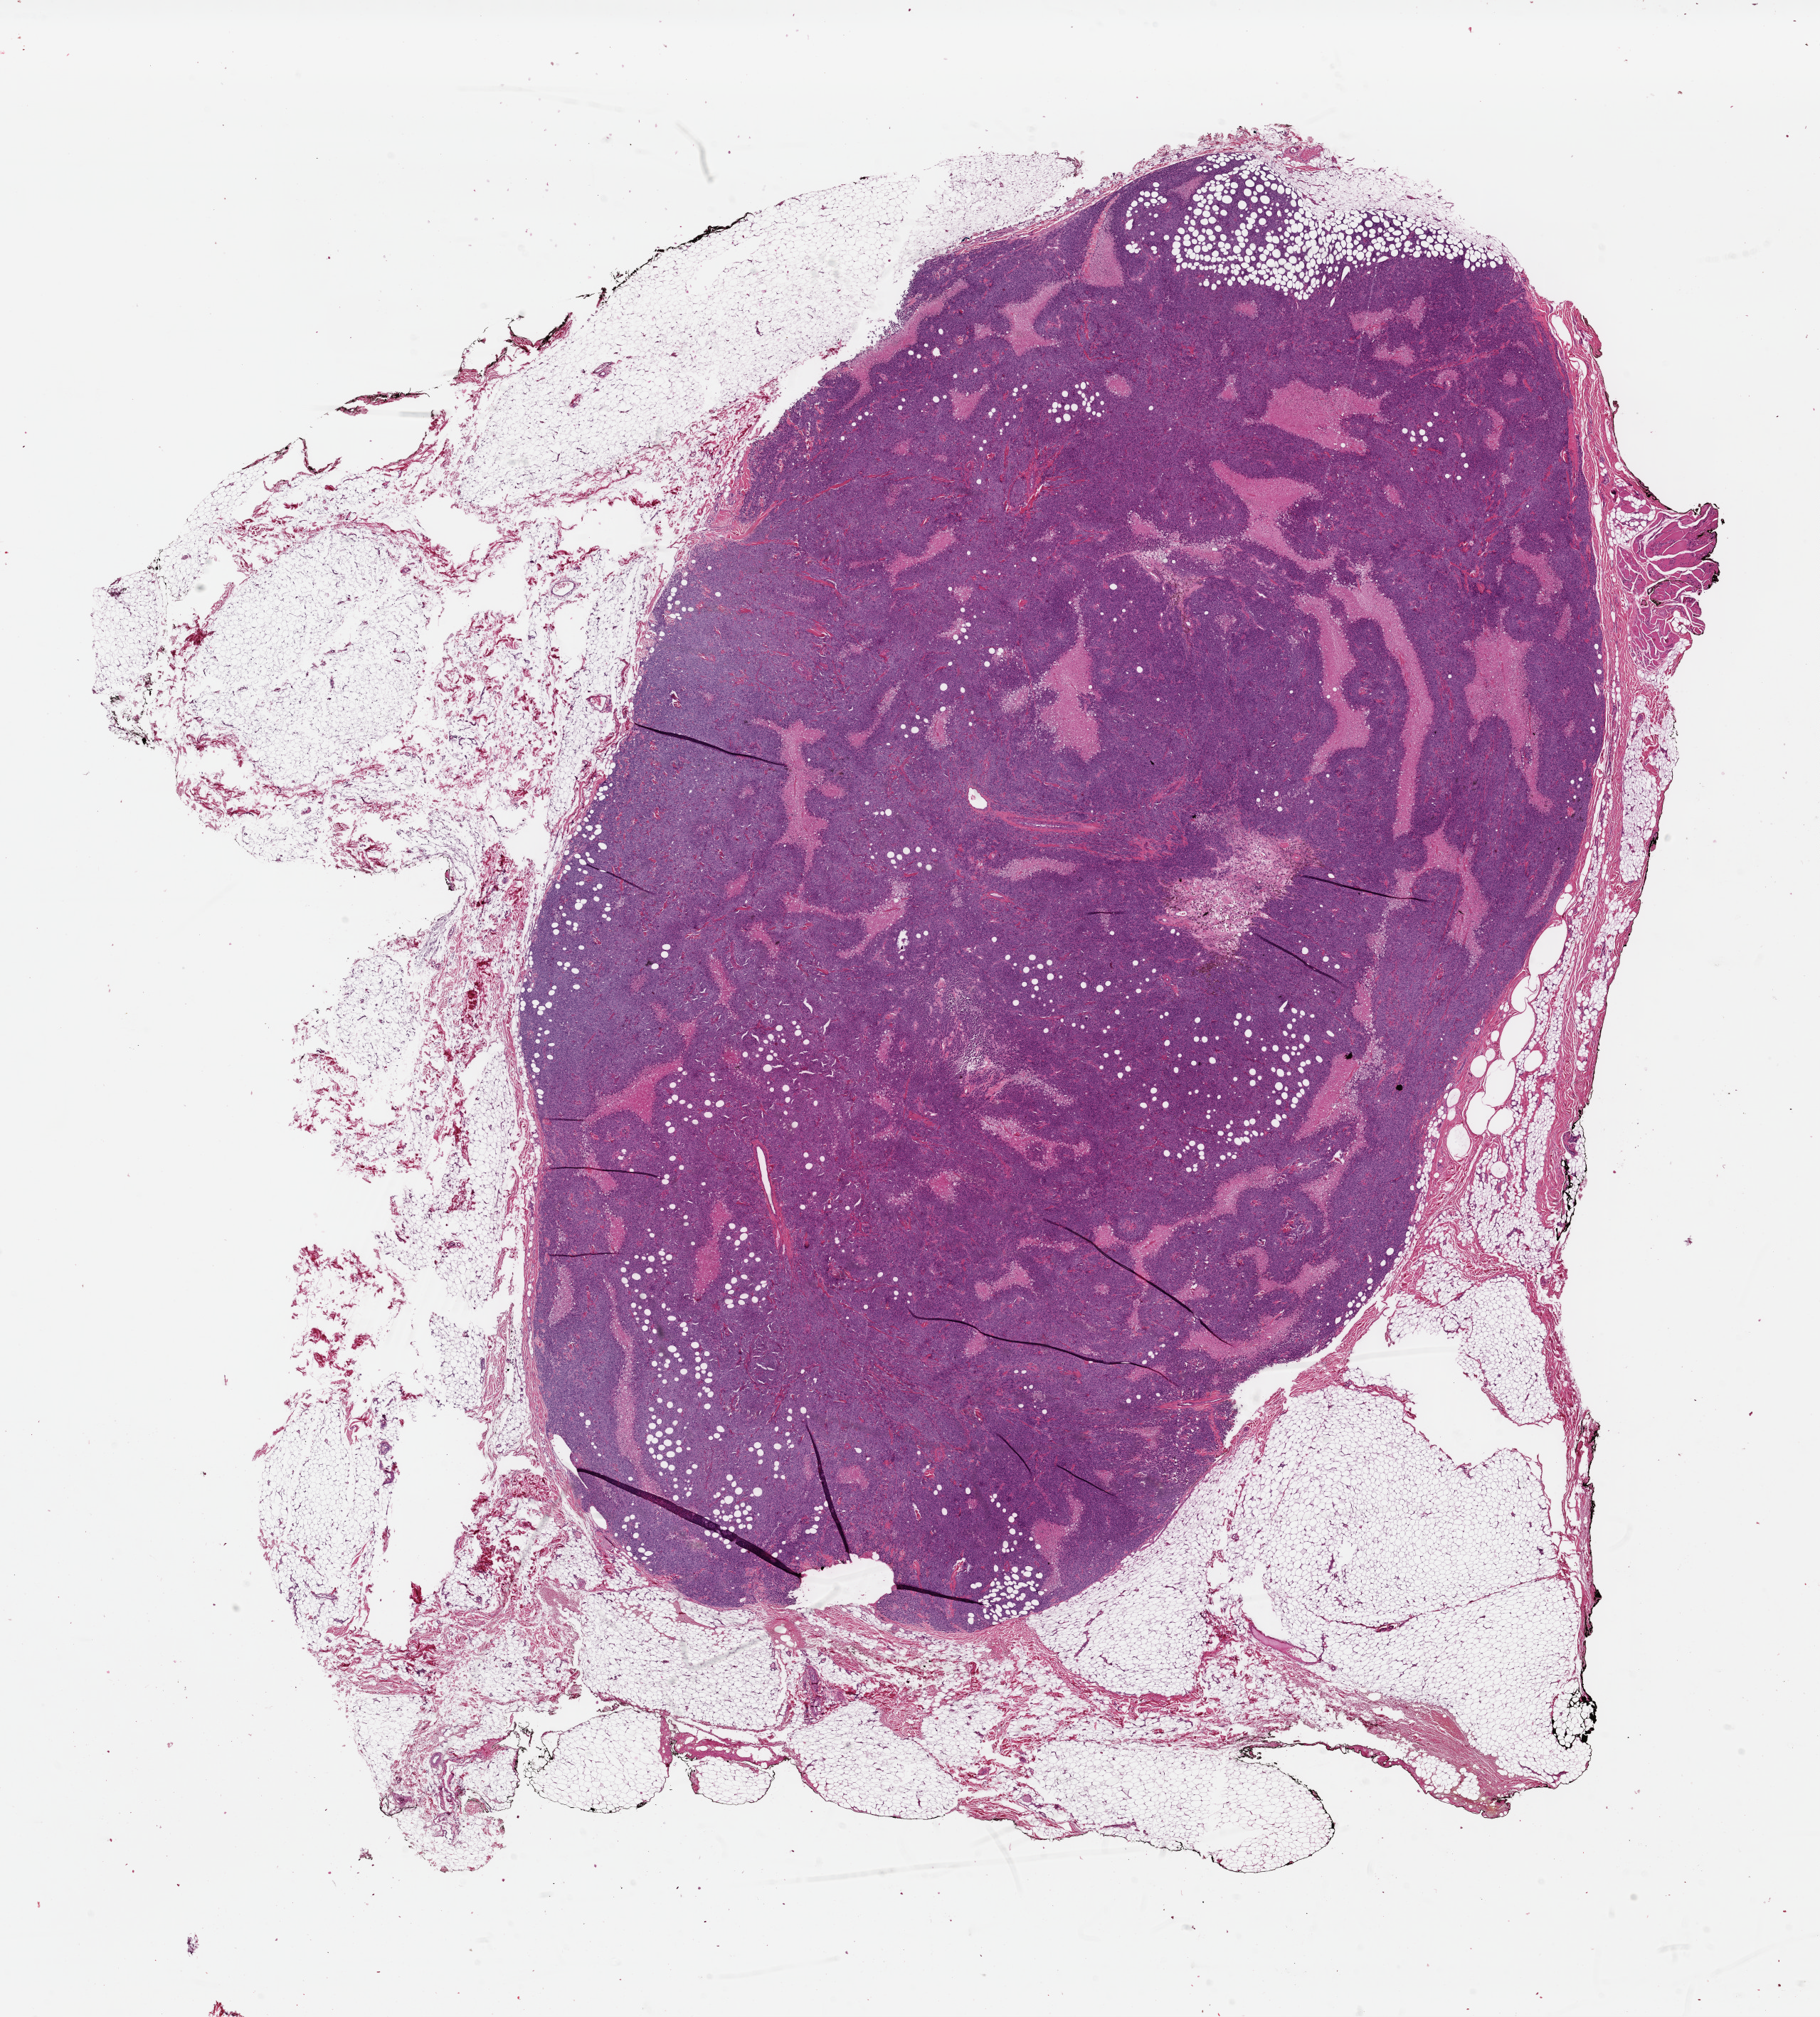
Digitized H&E tissue section (whole slide), whole scanned area (about 20.1 x 22.3 mm, slide scanned at 40x) shown as a low-resolution overview, FFPE section, primary tumour sample from the skin. Patient: male, age at initial diagnosis 59 years.
Pathologic diagnosis: Malignant melanoma, NOS.